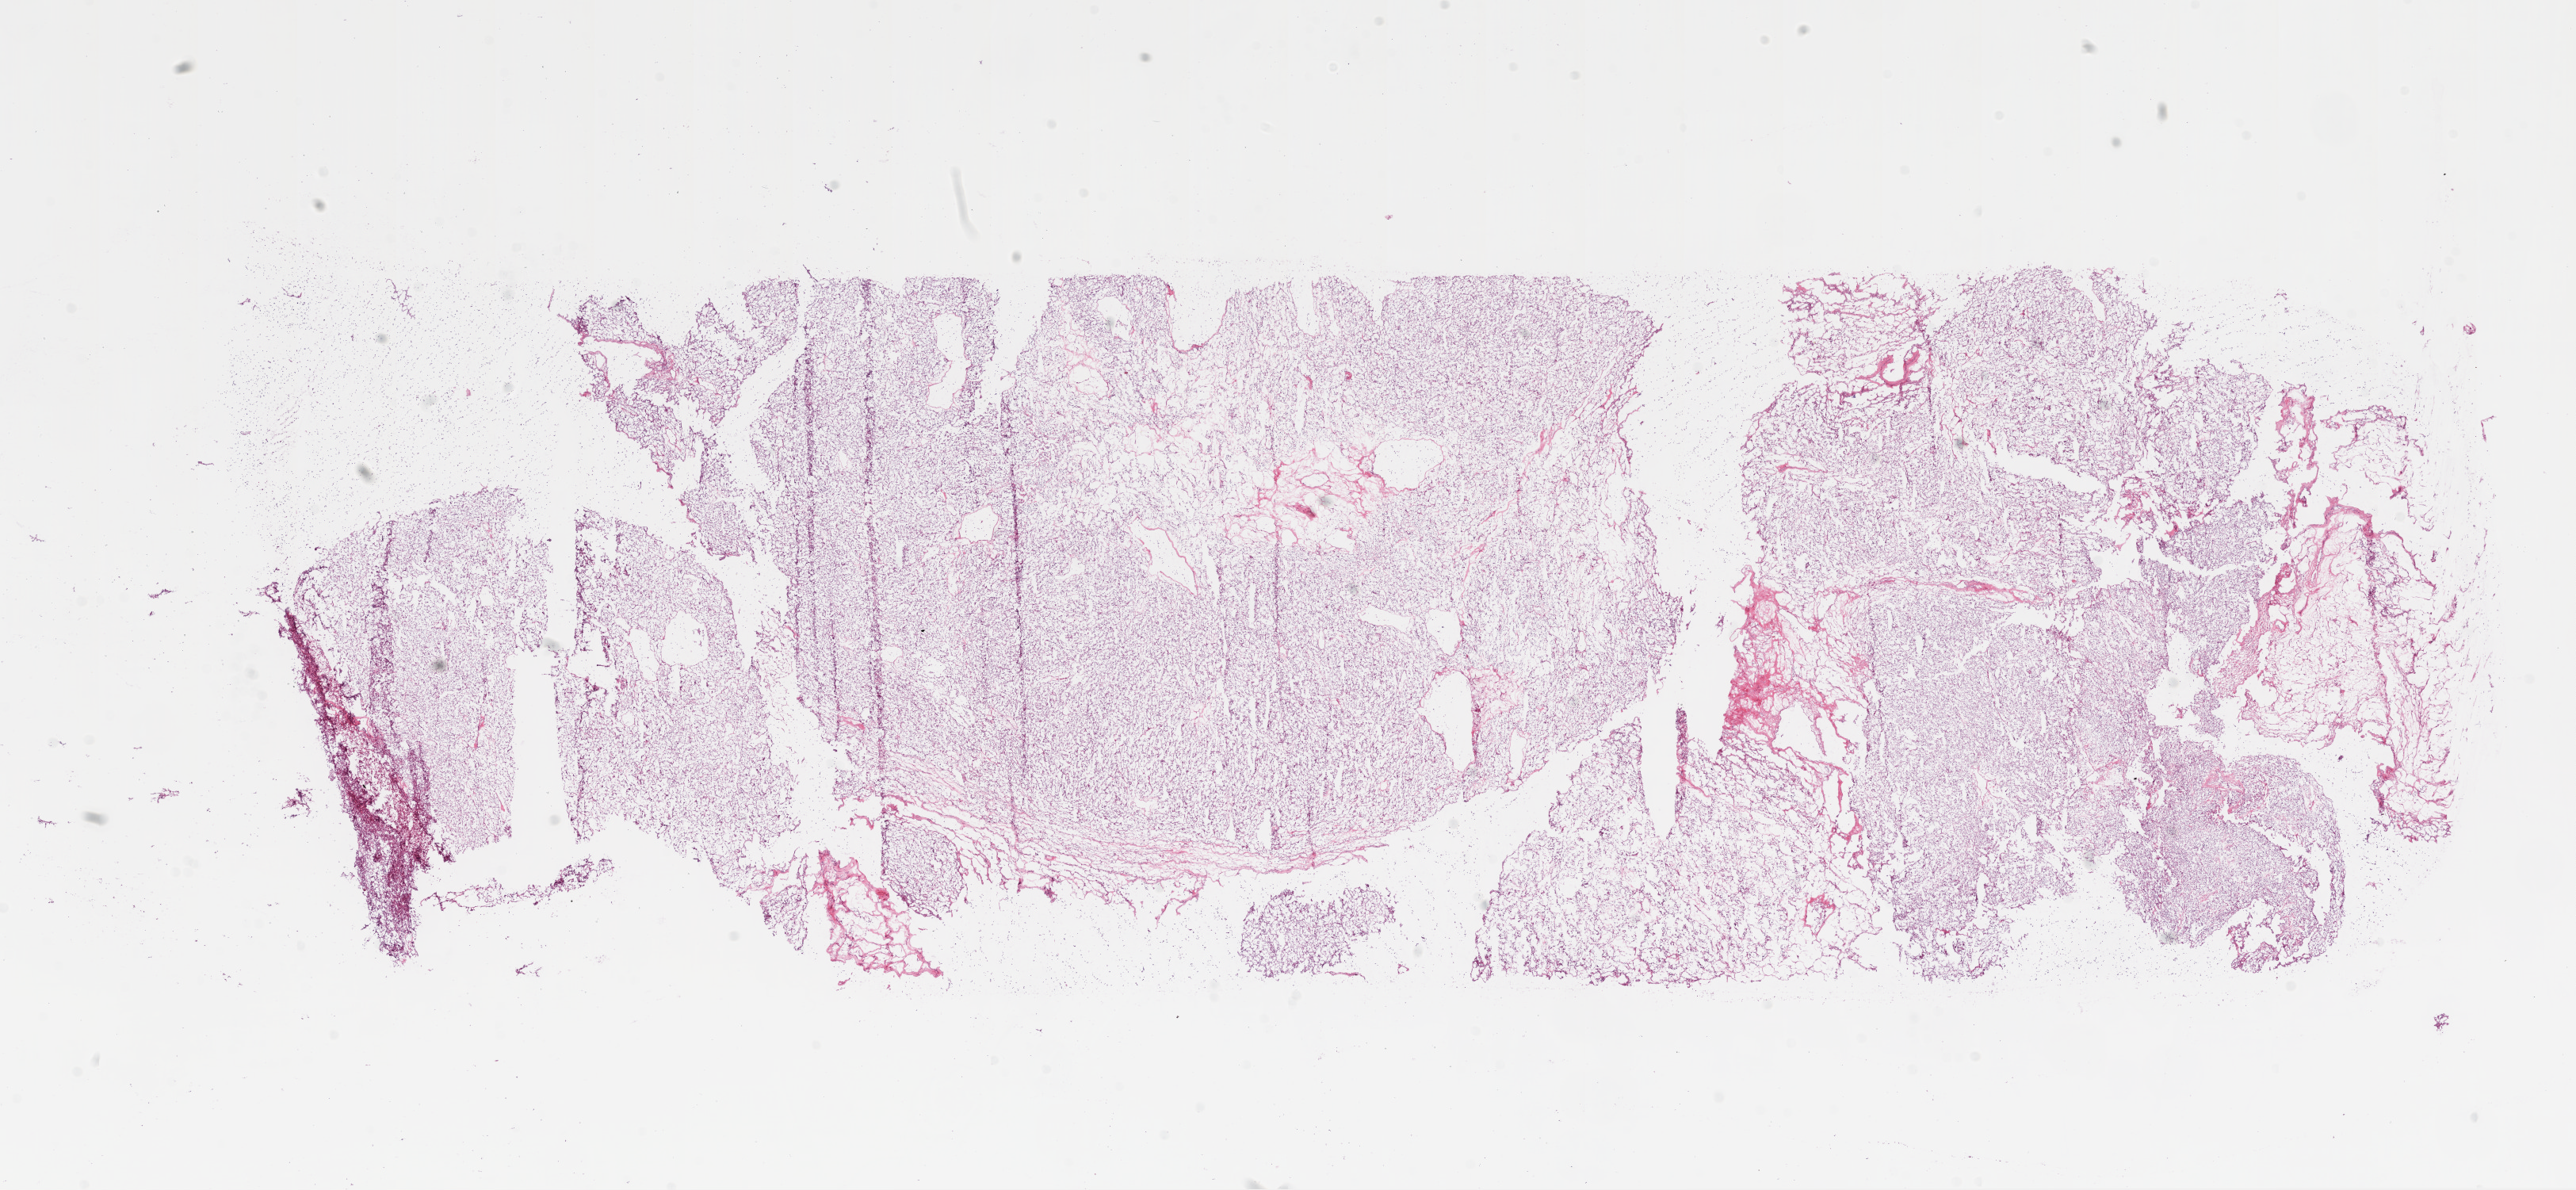
Digitized H&E-stained tissue section (whole slide) — a low-resolution overview of the entire scanned area, about 26.1 x 12.0 mm, frozen section, sample: primary tumour, kidney. Female patient; age at initial diagnosis 49 years. Histologic grade: G2 (moderately differentiated). Composition of this section per pathologist review: tumour cells 95%, tumour nuclei 80%, normal cells 0%, stromal cells 5%, necrosis 0%.
AJCC pathologic stage: II (7th edition). Pathologic diagnosis: Clear cell adenocarcinoma, NOS. TNM: T2 N0 M0.